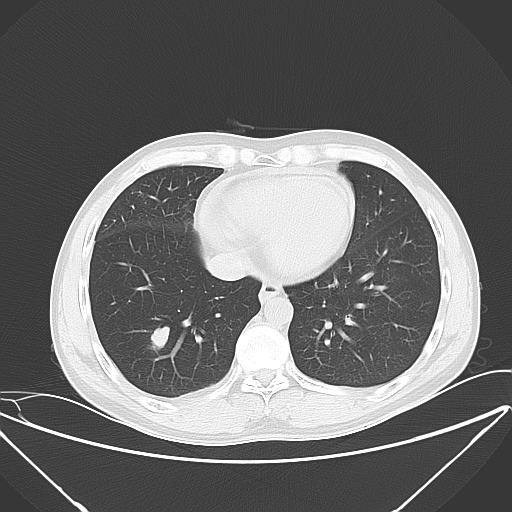
Chest CT, one axial slice. Slice 18 of 56 in the series (ordered by position). Lung window (W 1500 / L -600 HU). 5 mm slice thickness. 512 × 512 image matrix, field of view 397 × 397 mm. Patient: male, 42 years. Case-level facts recorded for this patient, not image findings: clinical TNM (as recorded): T1b N3 M1b; histopathological grade: G3.
Structures marked on this image (bounding box drawn by a radiologist):
- lung tumour (recorded histology: small cell carcinoma): bounding box [x1, y1, x2, y2] px = [139, 319, 177, 358]